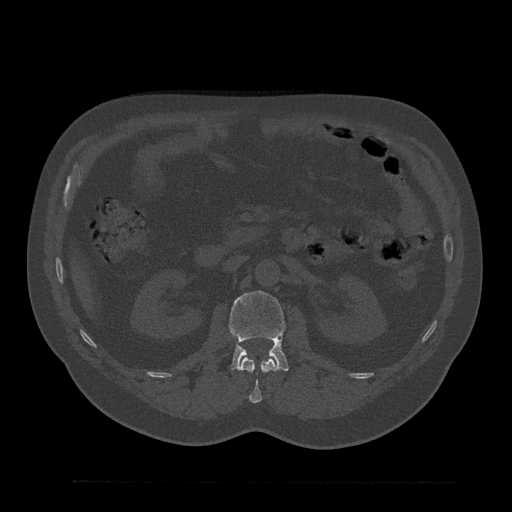
CT including the spine, one axial slice; position 126 of 797 along the scan axis; bone window (W 1800 / L 400 HU); 512 × 512 image matrix. Male patient, age 61 years. Case-level facts recorded for this patient, not image findings: primary cancer: prostate.
Structures marked on this image (semi-automatically segmented with operator editing):
- L1 vertebra: bounding box (x1, y1, x2, y2) in pixels: (240, 358, 279, 403)
- L2 vertebra: (229, 291, 288, 371)